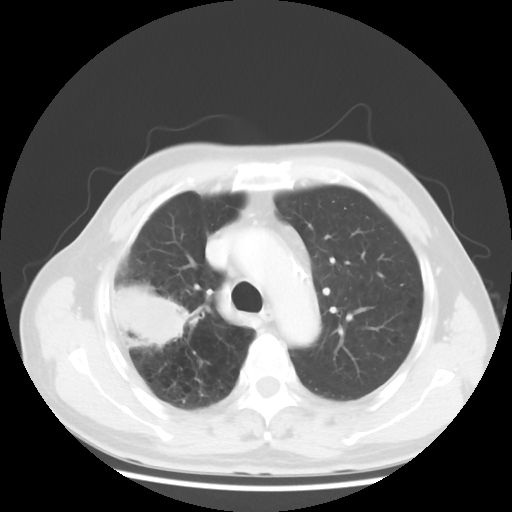
Chest CT, one axial slice; slice 36 of 50 in the series (ordered by position); reconstruction kernel STANDARD; 120 kVp; lung window (W 1500 / L -600 HU); 5 mm slice thickness; 512 × 512 image matrix, field of view 360 × 360 mm. Patient: male, 69 years. From the clinical record (not read from this slice): clinical TNM (as recorded): T3 N0 M0.
Annotated regions visible in this slice (bounding box drawn by a radiologist):
- lung tumour (recorded histology: adenocarcinoma): bounding box <108,271,198,355> (left, top, right, bottom; pixels)